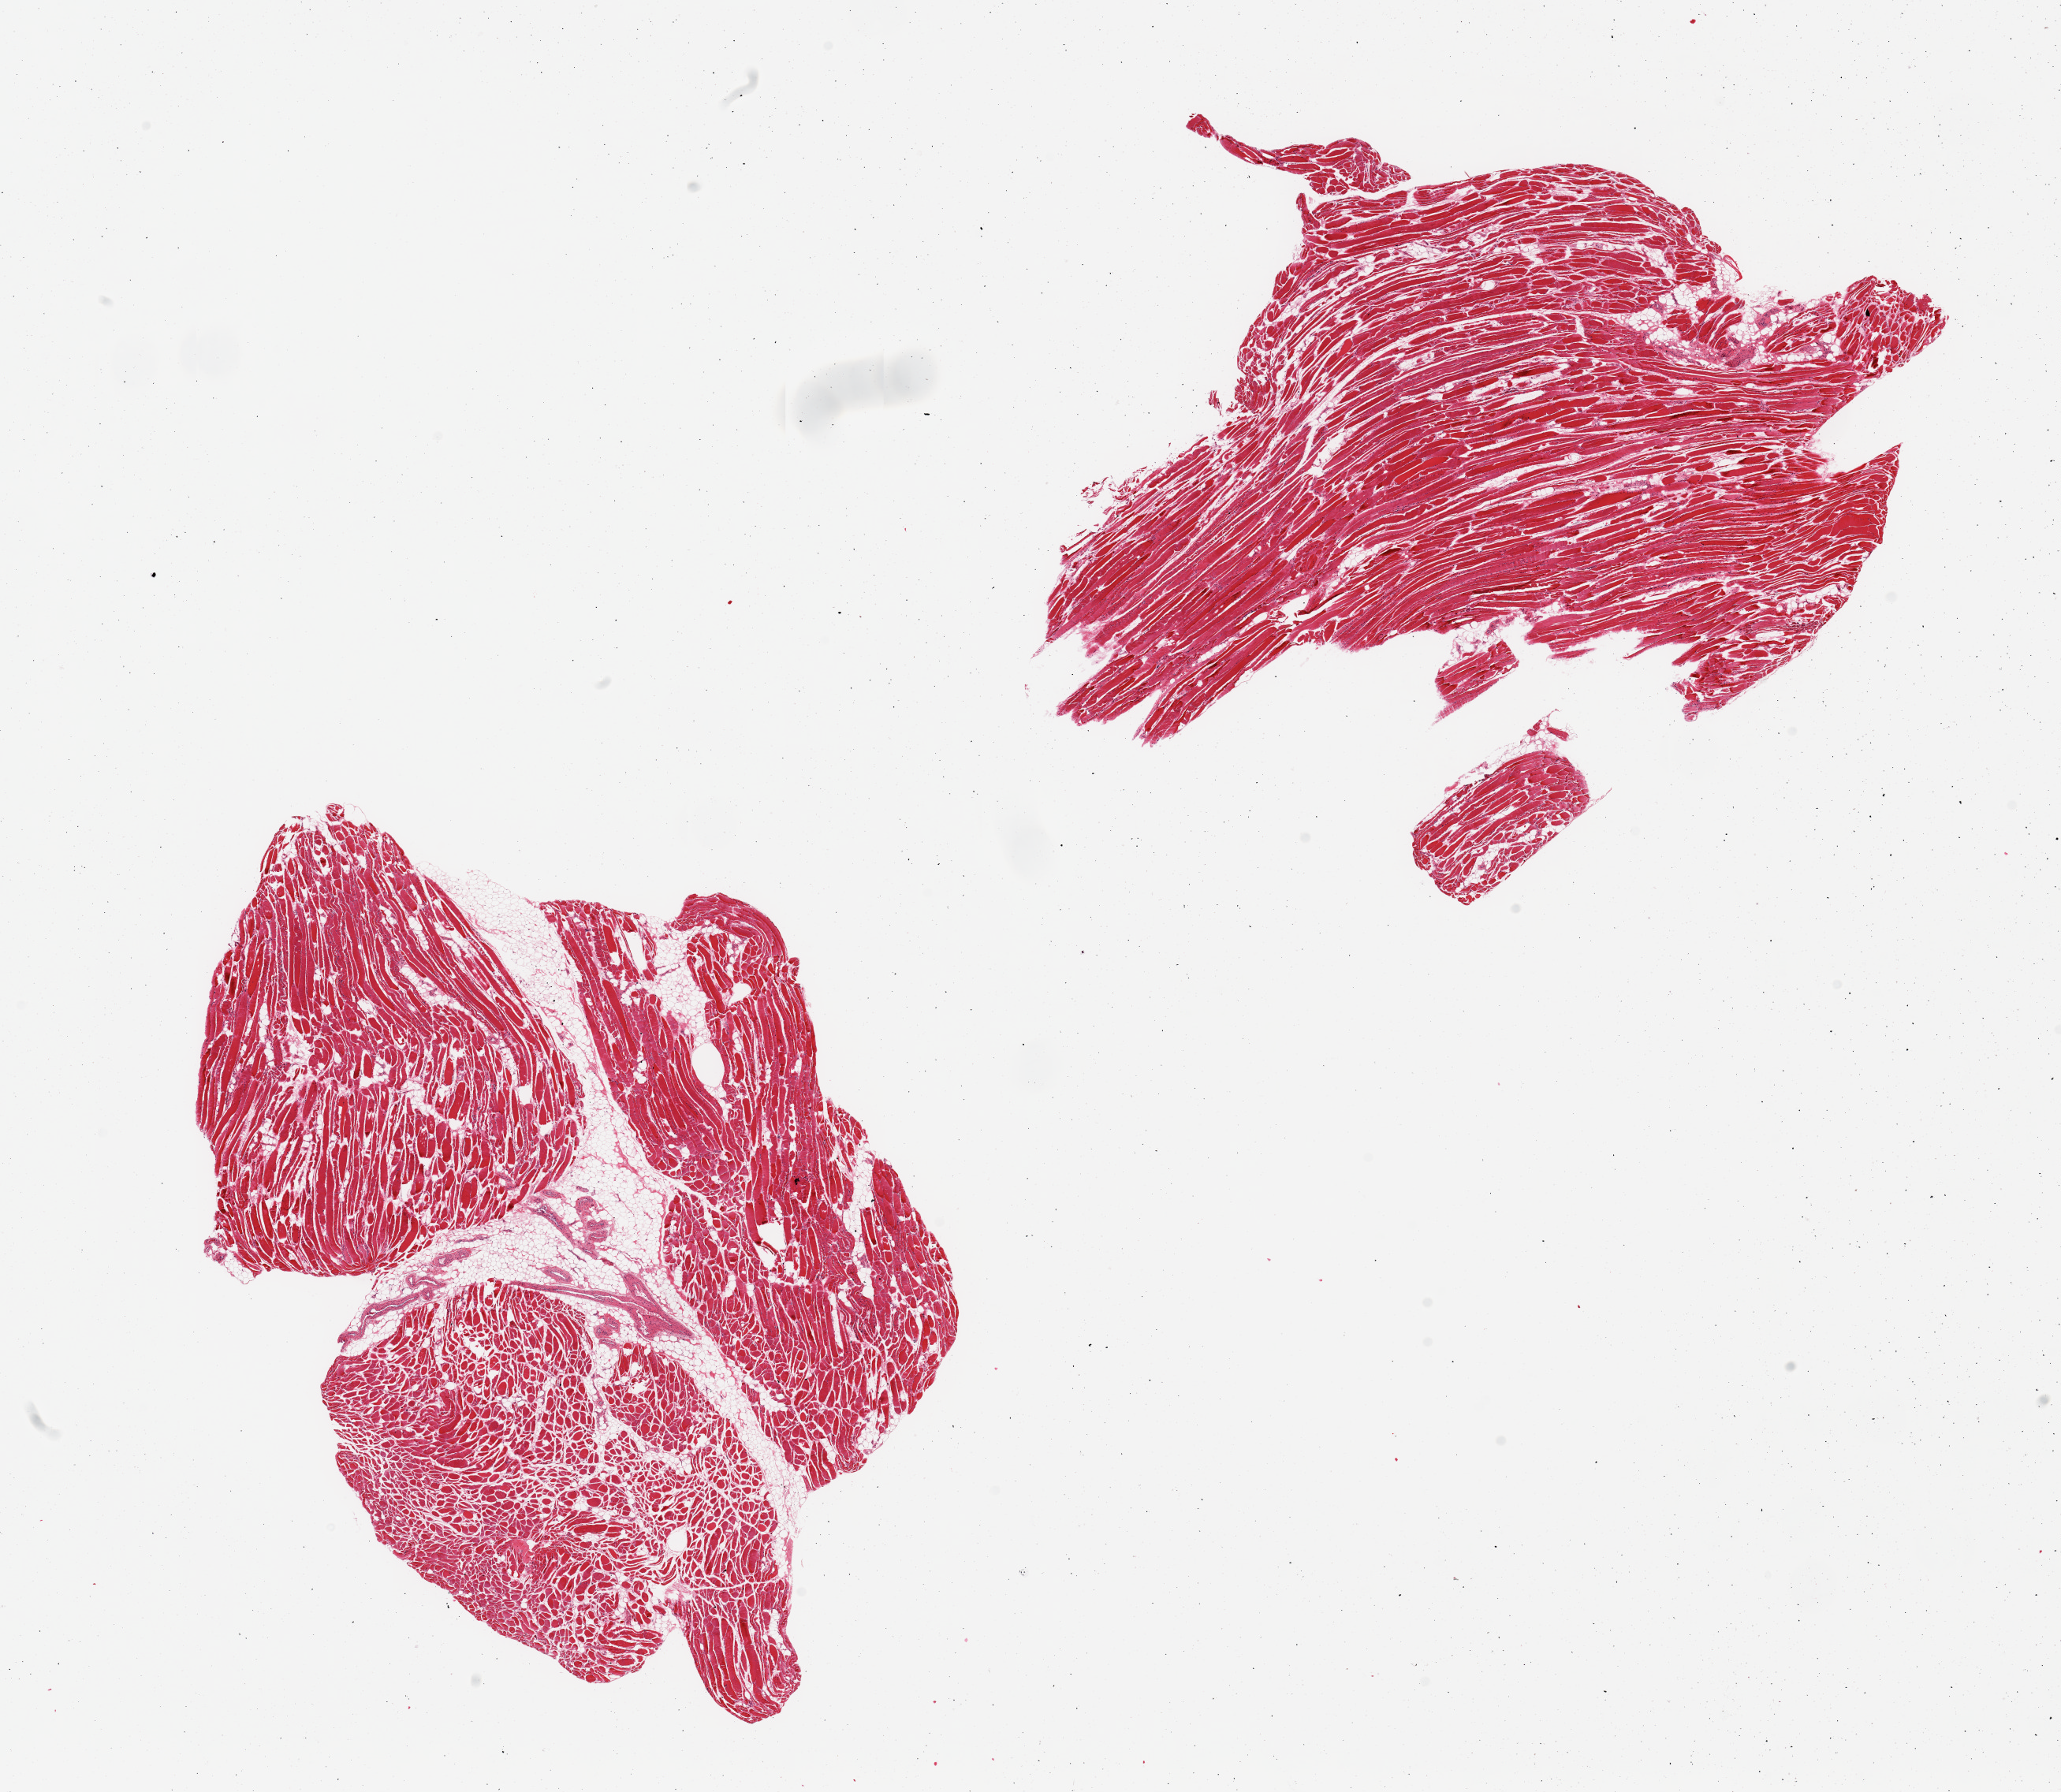
Whole-slide image, haematoxylin and eosin stain, brightfield, shown as a low-resolution overview of the whole scanned area (about 20.7 x 18.0 mm). PAXgene-fixed paraffin-embedded (PFPE) section. Sampled site (target tissue): skeletal muscle. Donor tissue sample. Donor sex: female.
- reviewer comment on this tissue sample: 2 pieces; 10% internal fat in 1 piece